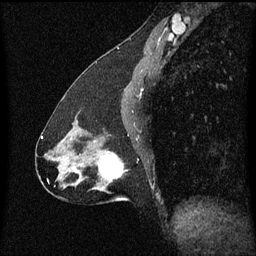
Breast MRI (dynamic contrast-enhanced), one sagittal slice. Position 29 of 60 along the scan axis. Dynamic contrast-enhanced series, image 2 of 3 at this slice position (ordered by acquisition). 1.5 T. TE 4.2 ms, TR 8.4 ms. 2 mm slice thickness. 256 × 256 image matrix. Female patient, age 47 years.
Outlined on this slice (semi-automatically segmented with operator editing):
- analysis volume of interest (the breast-tissue region the enhancement analysis was run in; not a lesion): bounding box <81,140,123,193> (left, top, right, bottom; pixels)
- tumour enhancement mask (voxels above the 70 % enhancement threshold inside the analysis volume of interest): <99,156,123,181>